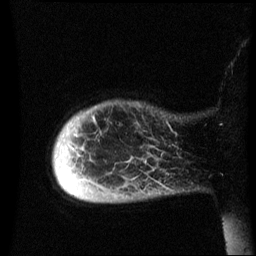
Breast MRI (dynamic contrast-enhanced), one sagittal slice. Position 6 of 60 along the scan axis. Dynamic contrast-enhanced series, image 2 of 3 at this slice position (ordered by acquisition). 1.5 T. TE 4.2 ms, TR 8.4 ms. 2.5 mm slice thickness. 256 × 256 image matrix. Female patient, age 49 years.
Annotated regions visible in this slice (semi-automatic segmentation, software-assisted and operator-edited):
- analysis volume of interest (the breast-tissue region the enhancement analysis was run in; not a lesion): box from (x=54, y=102) to (x=185, y=203) px
- tumour enhancement mask (voxels above the 70 % enhancement threshold inside the analysis volume of interest): (x=94, y=118)–(x=97, y=123)